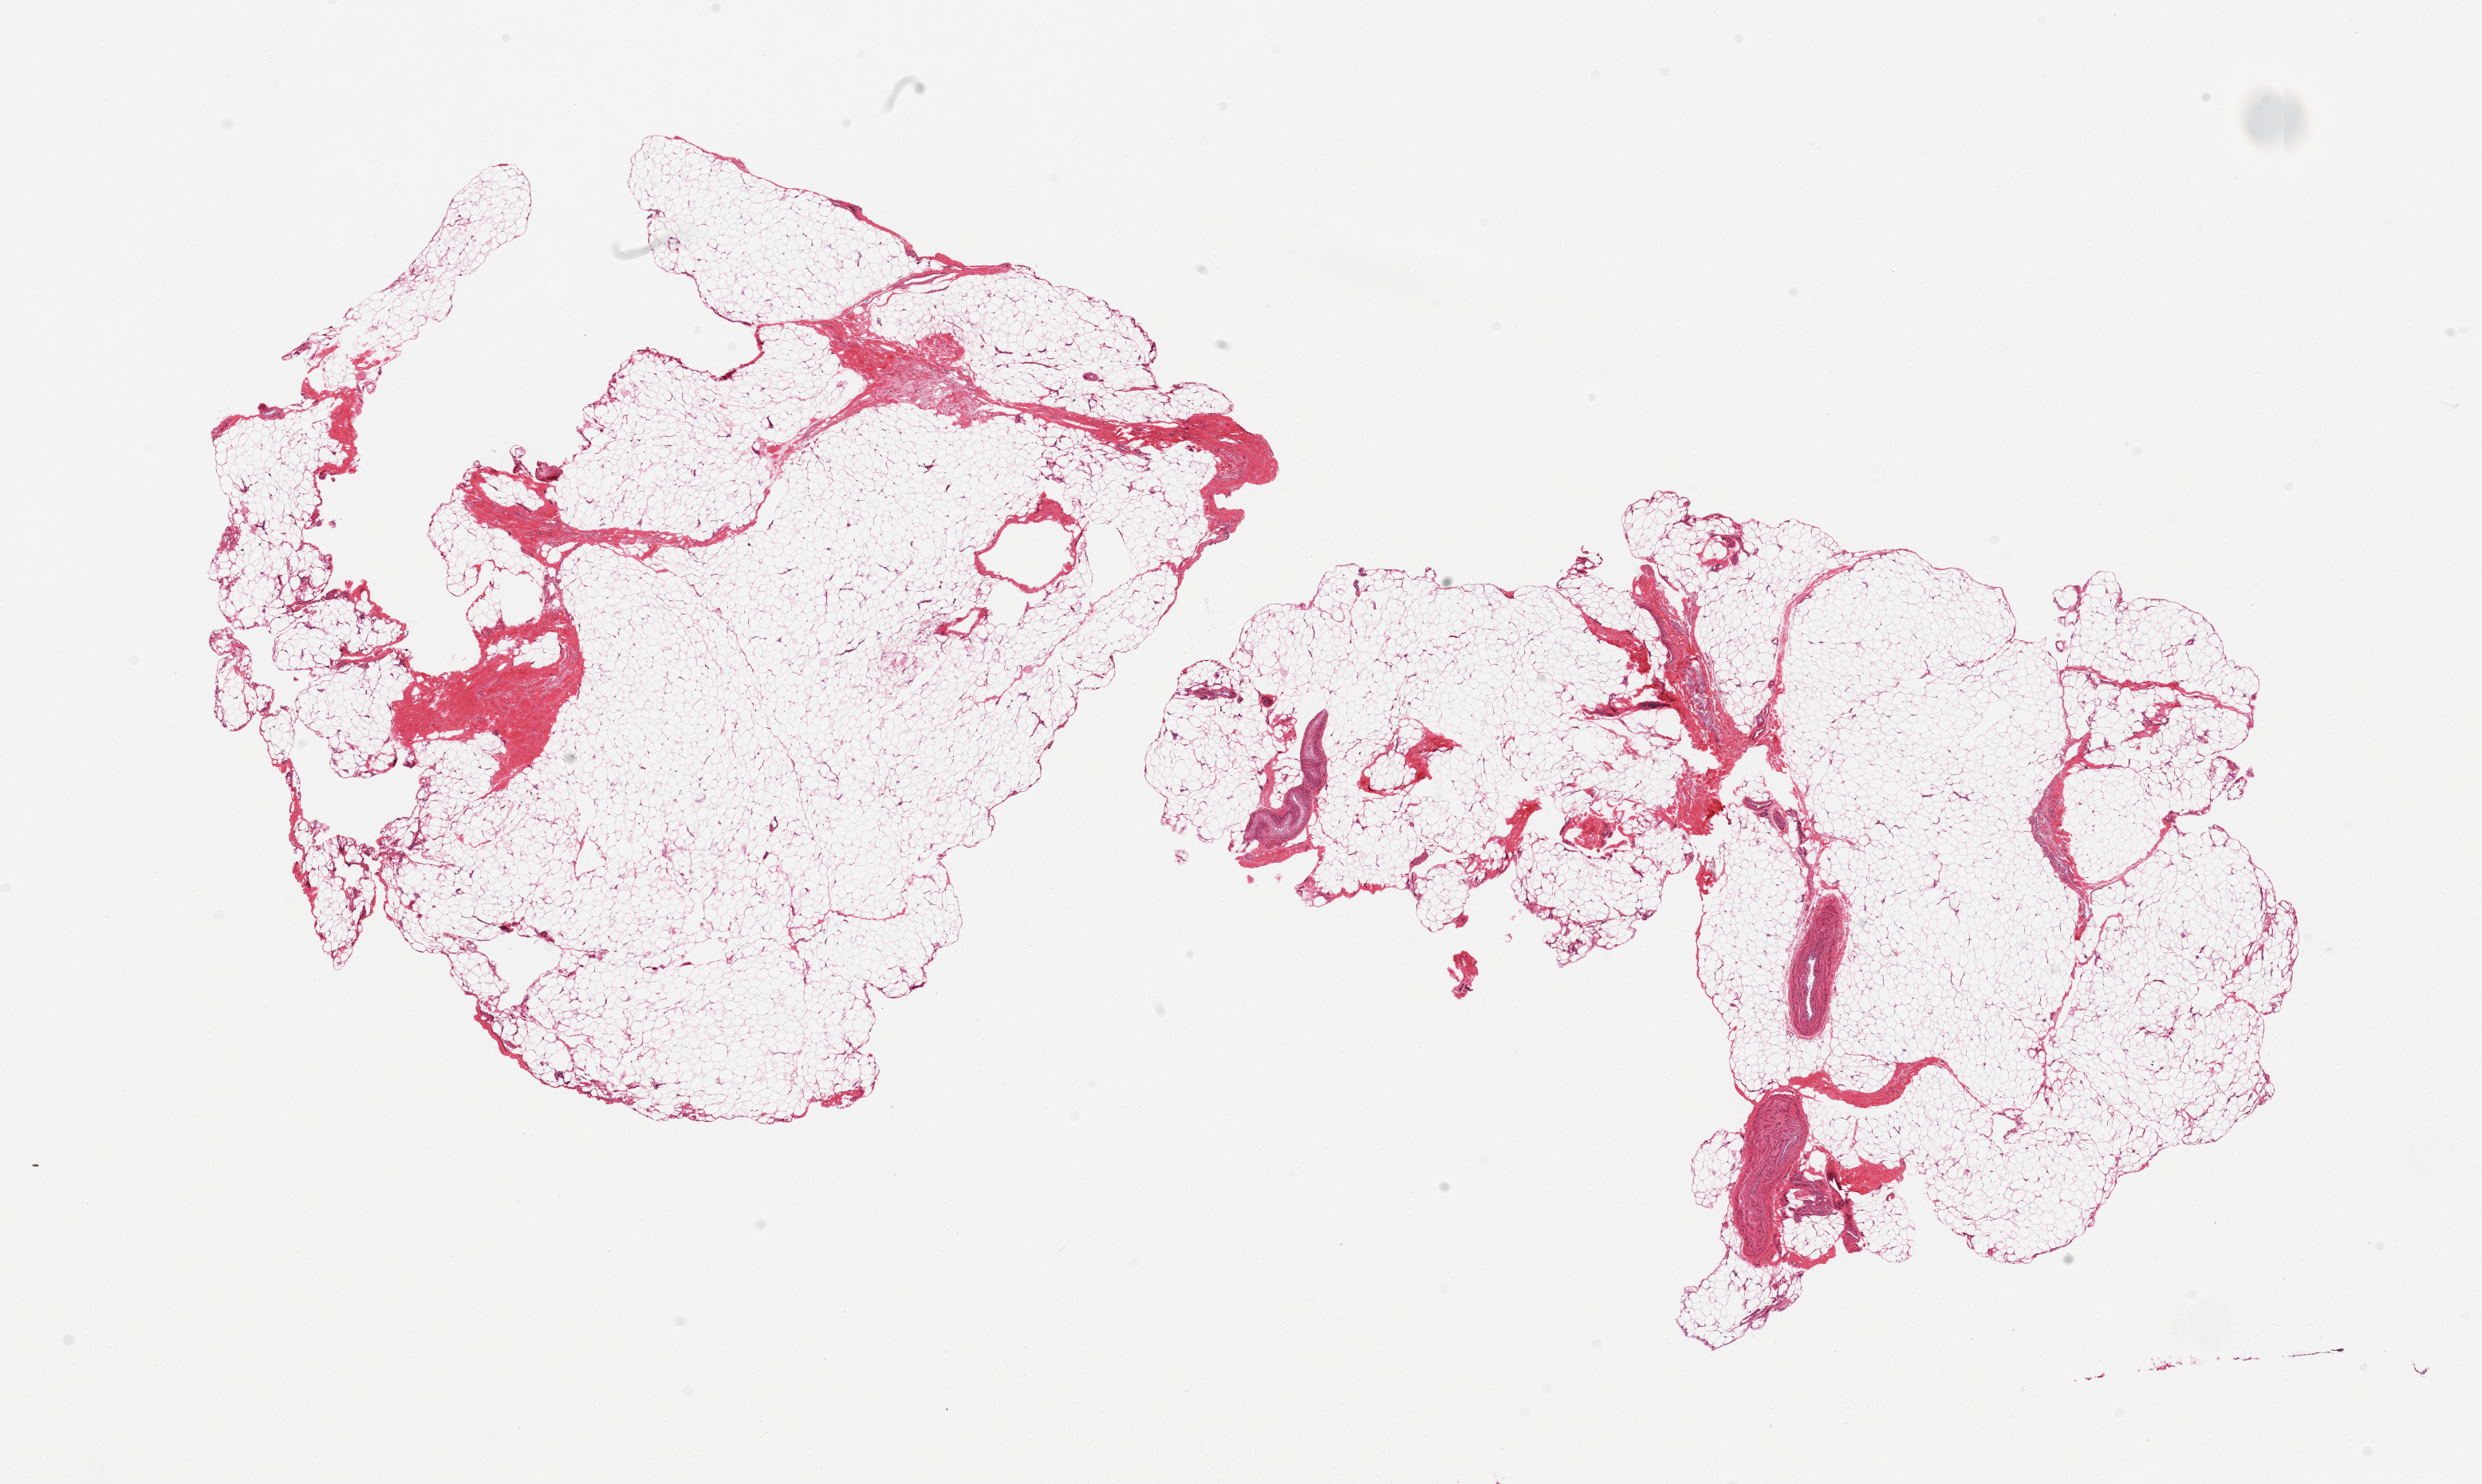
Hematoxylin and eosin (H&E) whole-slide image, brightfield, whole scanned area (about 24.6 x 14.7 mm) shown as a low-resolution overview, PAXgene-fixed, paraffin-embedded tissue, sampled site (target tissue): adipose tissue, tissue donor sample. Male donor.
Pathologist's review note for this sample: 2 pieces; 5% fibrous content.